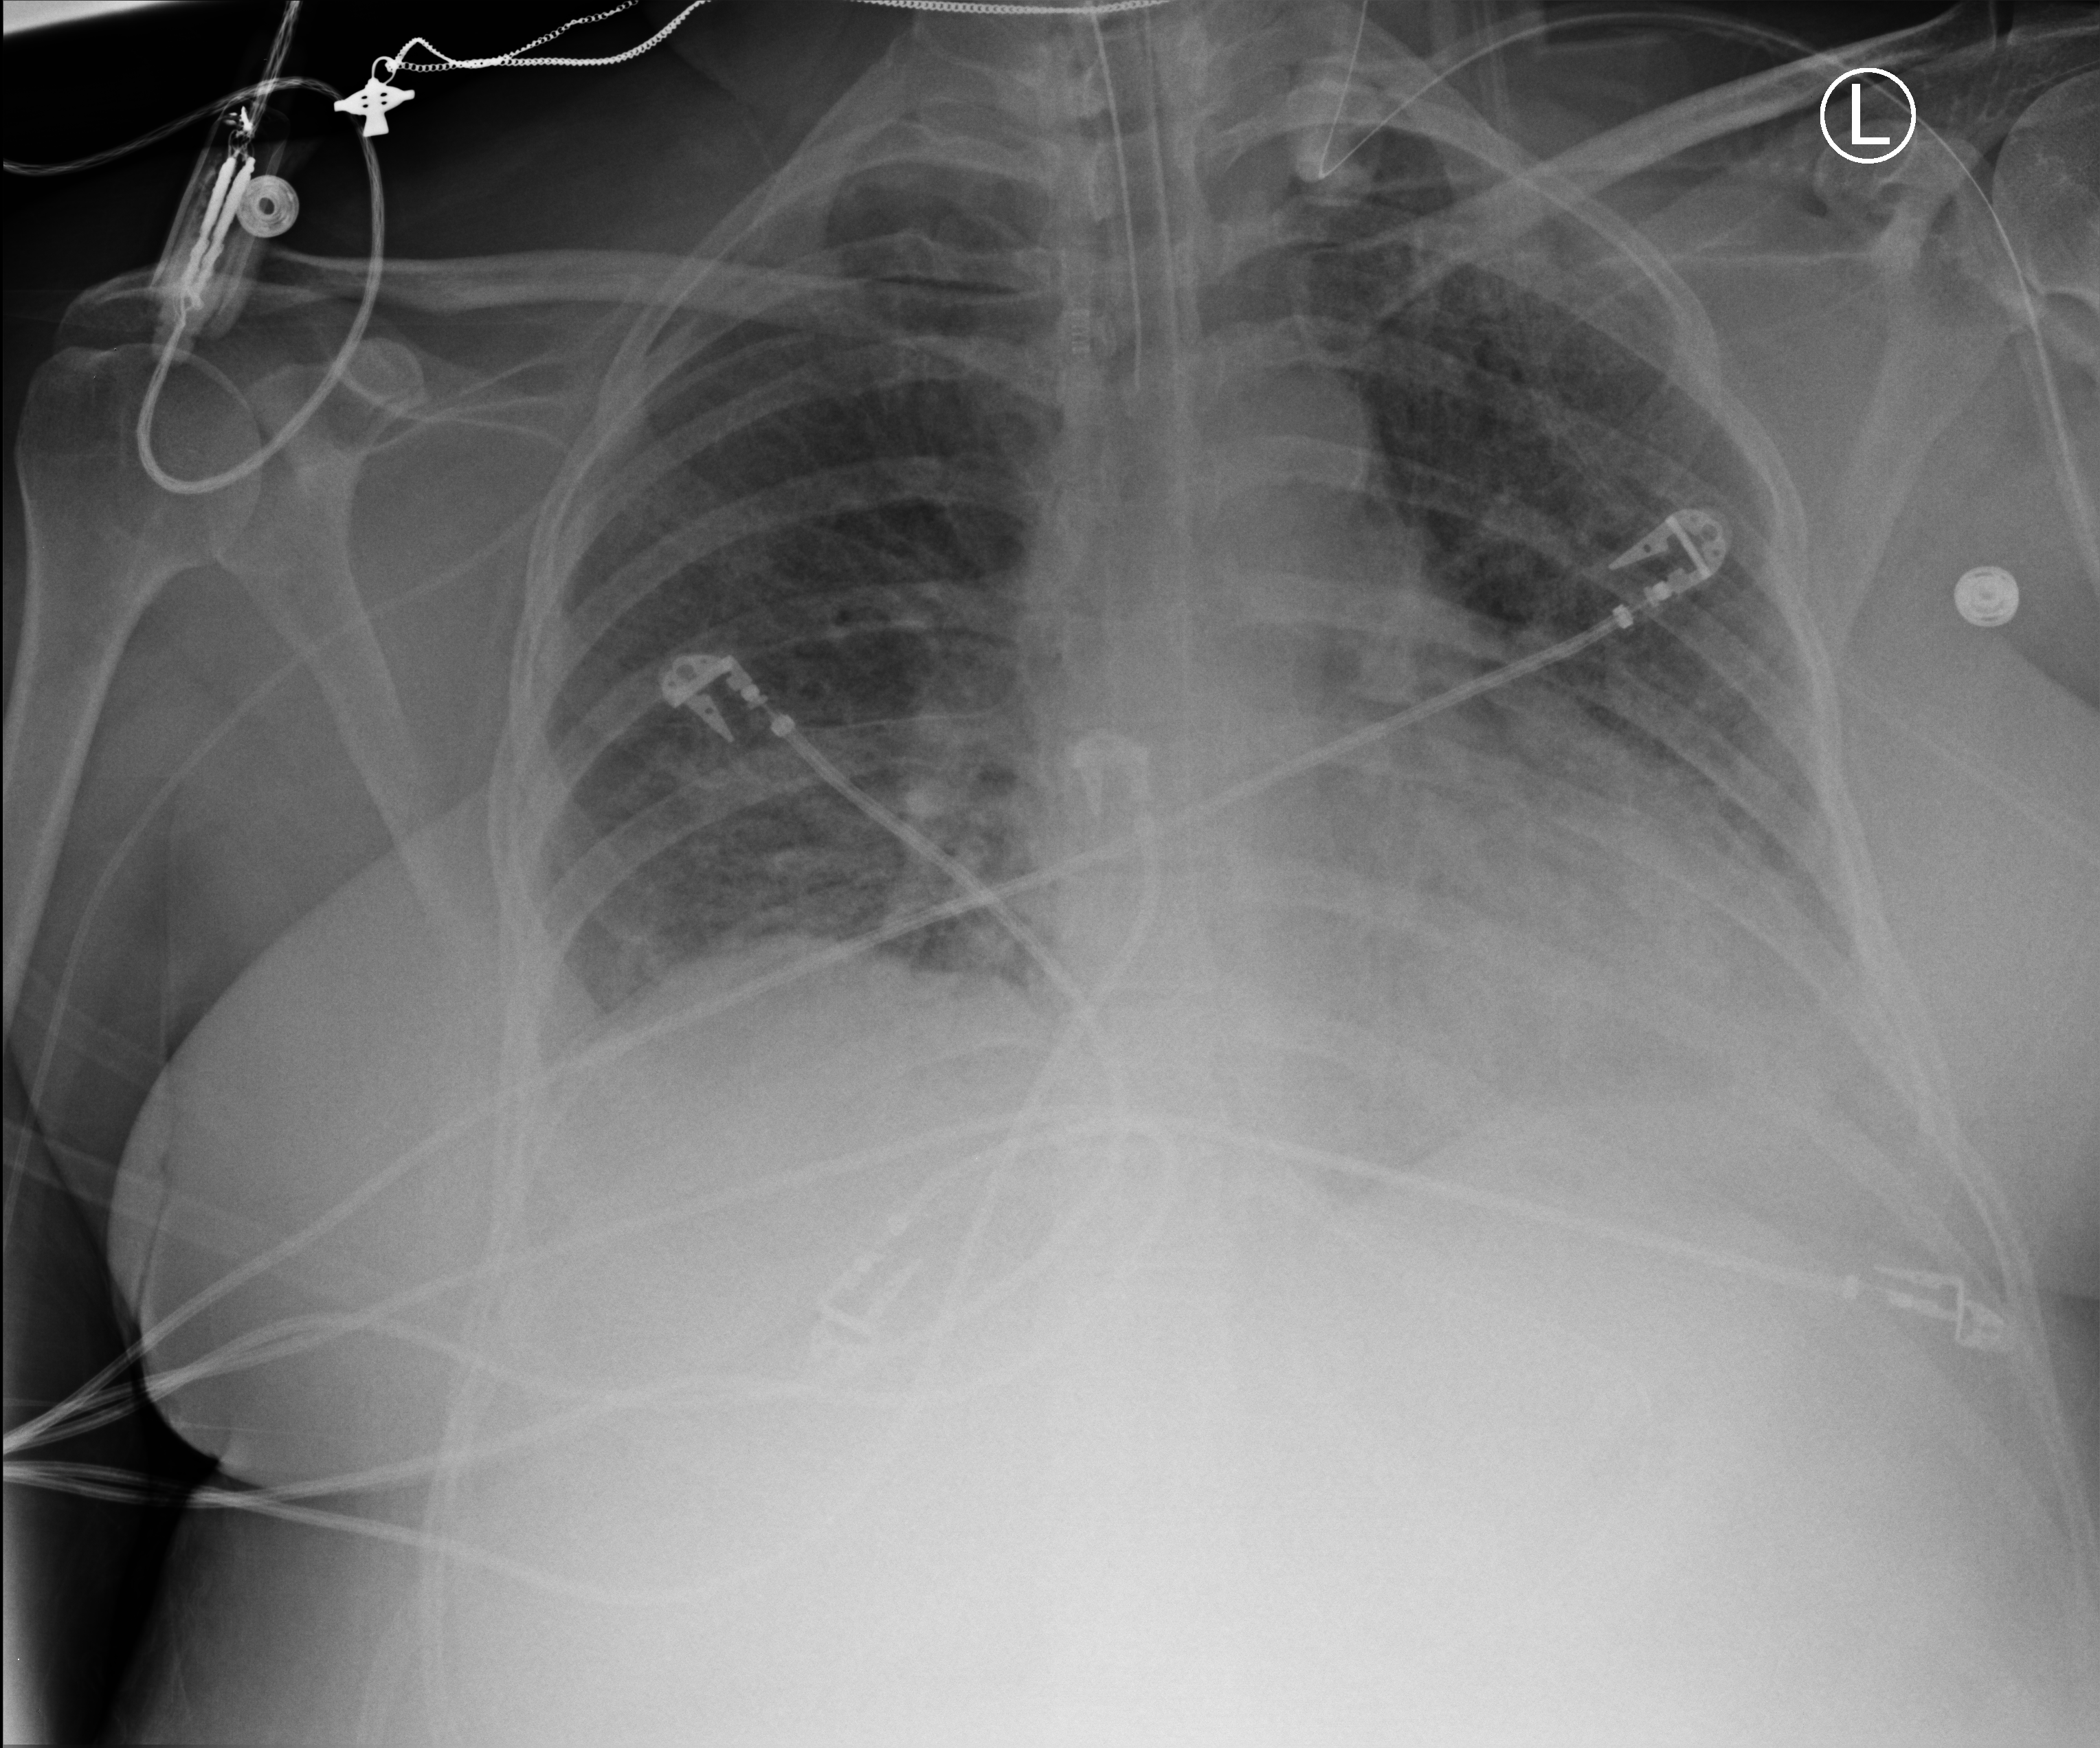
Chest X-ray (portable); anteroposterior (AP) projection. Female patient hospitalised with COVID-19, age 18–59 years.
Admission-level facts for this patient (not findings on this image; timing relative to this image not recorded): admitted to intensive care during this hospital stay: yes.